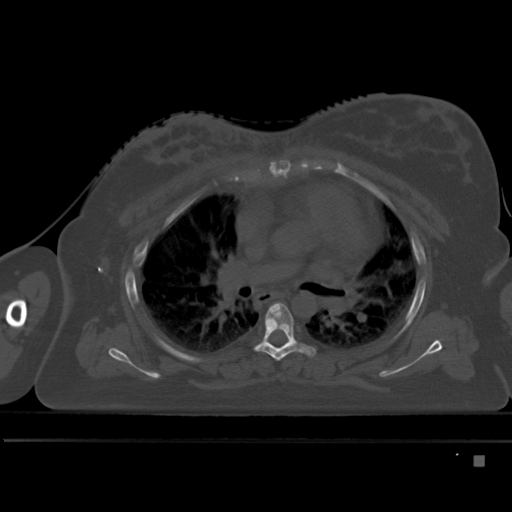
CT including the spine, one axial slice. Position 320 of 495 along the scan axis. Bone window (W 1800 / L 400 HU). 1.5 mm slice thickness. 512 × 512 image matrix. Patient: female, 33 years. From the clinical record (not read from this slice): primary cancer: breast.
Outlined on this slice (semi-automatically segmented with operator editing):
- T5 vertebra: bounding box [x1, y1, x2, y2] px = [255, 303, 315, 361]